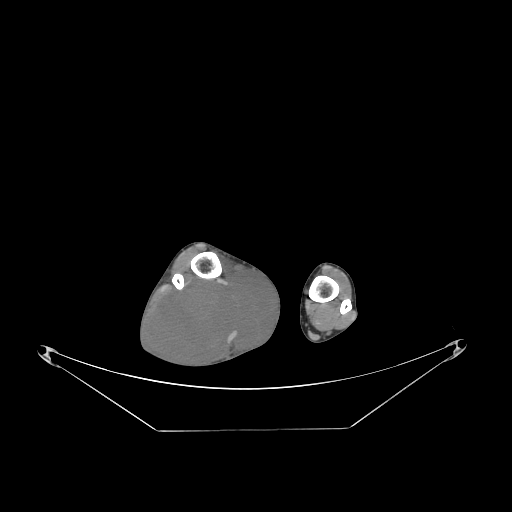
CT of an extremity soft-tissue mass (from a PET/CT study), one axial slice; slice 61 of 267 in the series (ordered by position); soft-tissue window (W 400 / L 40 HU); 512 × 512 image matrix, field of view 500 × 500 mm. Male patient. From the clinical record (not read from this slice): histological type: liposarcoma - round cell; grade: high; site of the primary tumour: right calf.
Structures marked on this image (expert contour drawn on MRI and transferred to this co-registered scan by the dataset authors):
- gross tumour volume (mass): bounding box <151,267,279,369> (left, top, right, bottom; pixels)